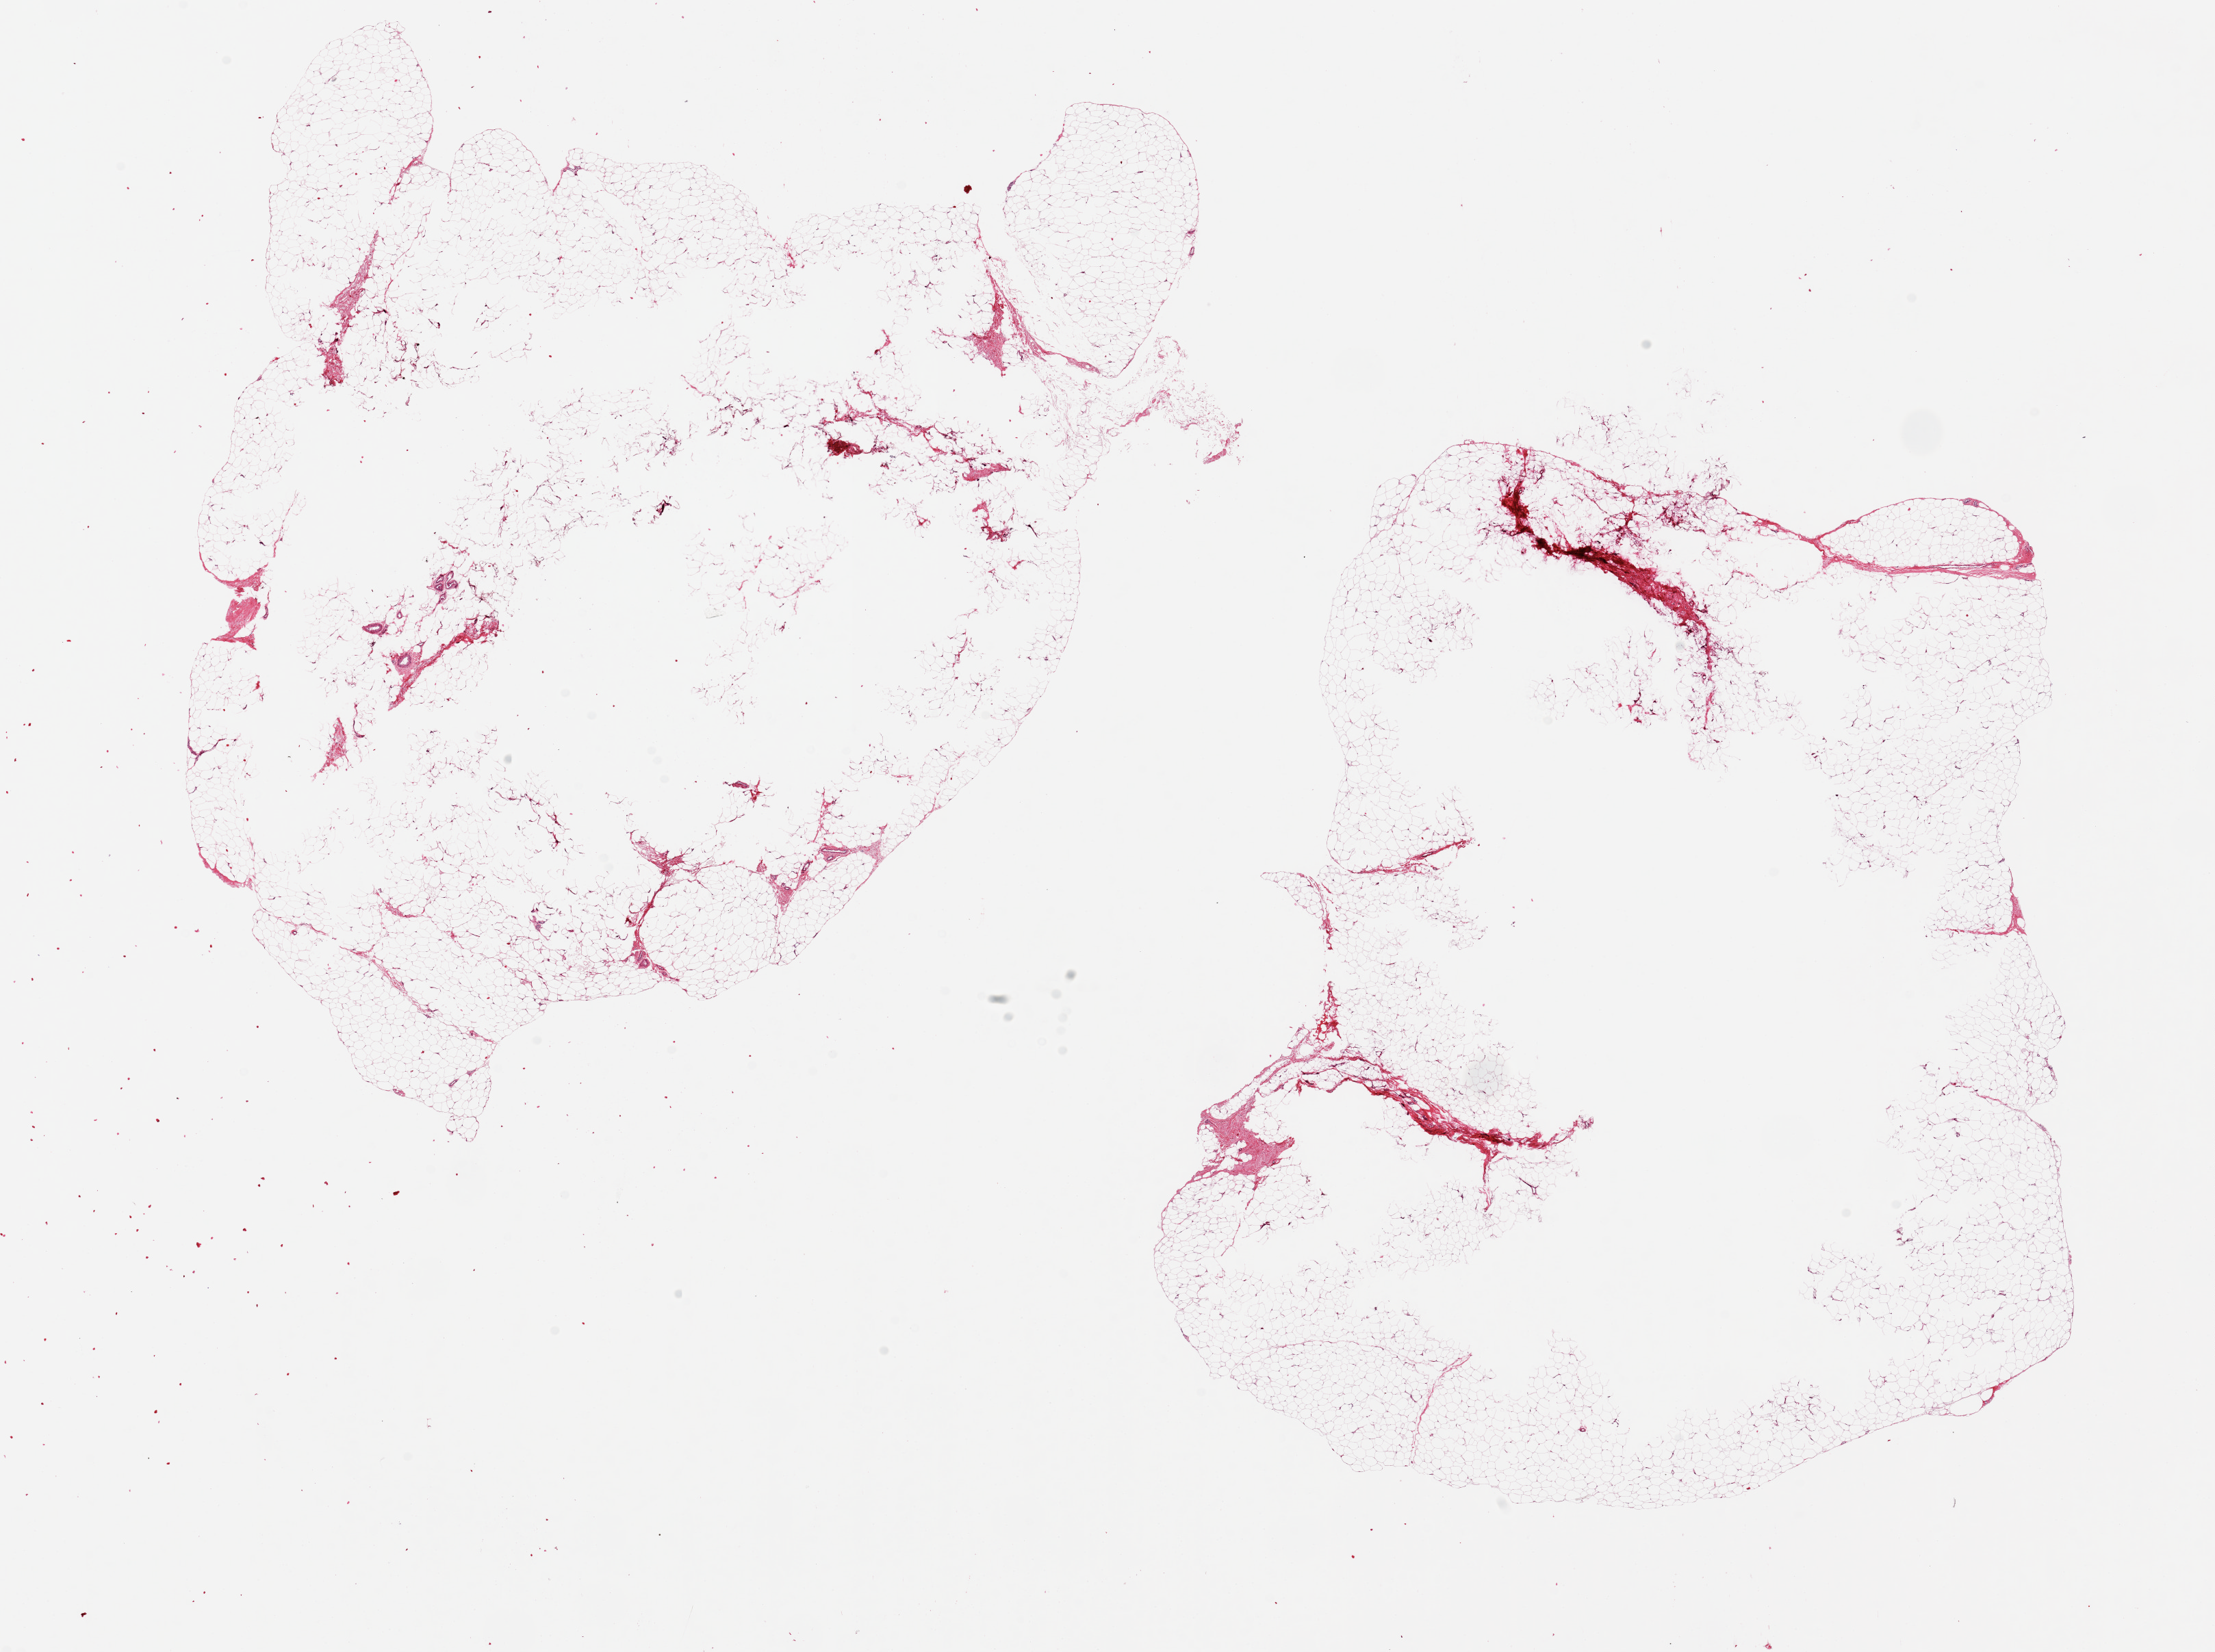
H&E whole-slide image — shown as a low-resolution overview of the whole scanned area (about 25.6 x 19.1 mm, acquisition: 20x scan). PAXgene-fixed, paraffin-embedded tissue. Target tissue: adipose tissue. Donor tissue sample. Female donor.
Reviewer comment on this tissue sample: 2 pieces, 14x13 & 13x11mm.